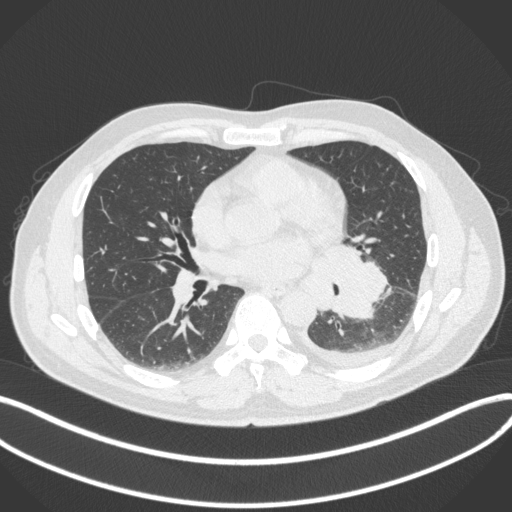
Chest CT, one axial slice; position 175 of 350 along the scan axis; reconstruction kernel B31f; lung window (W 1500 / L -600 HU); 512 × 512 image matrix, field of view 400 × 400 mm. Patient: male, 58 years. From the clinical record (not read from this slice): clinical TNM (as recorded): T3 N1 M1b.
Structures marked on this image (rectangle marked by the reading radiologist):
- lung tumour (recorded histology: small cell carcinoma): bounding box [x1, y1, x2, y2] px = [312, 240, 392, 324]